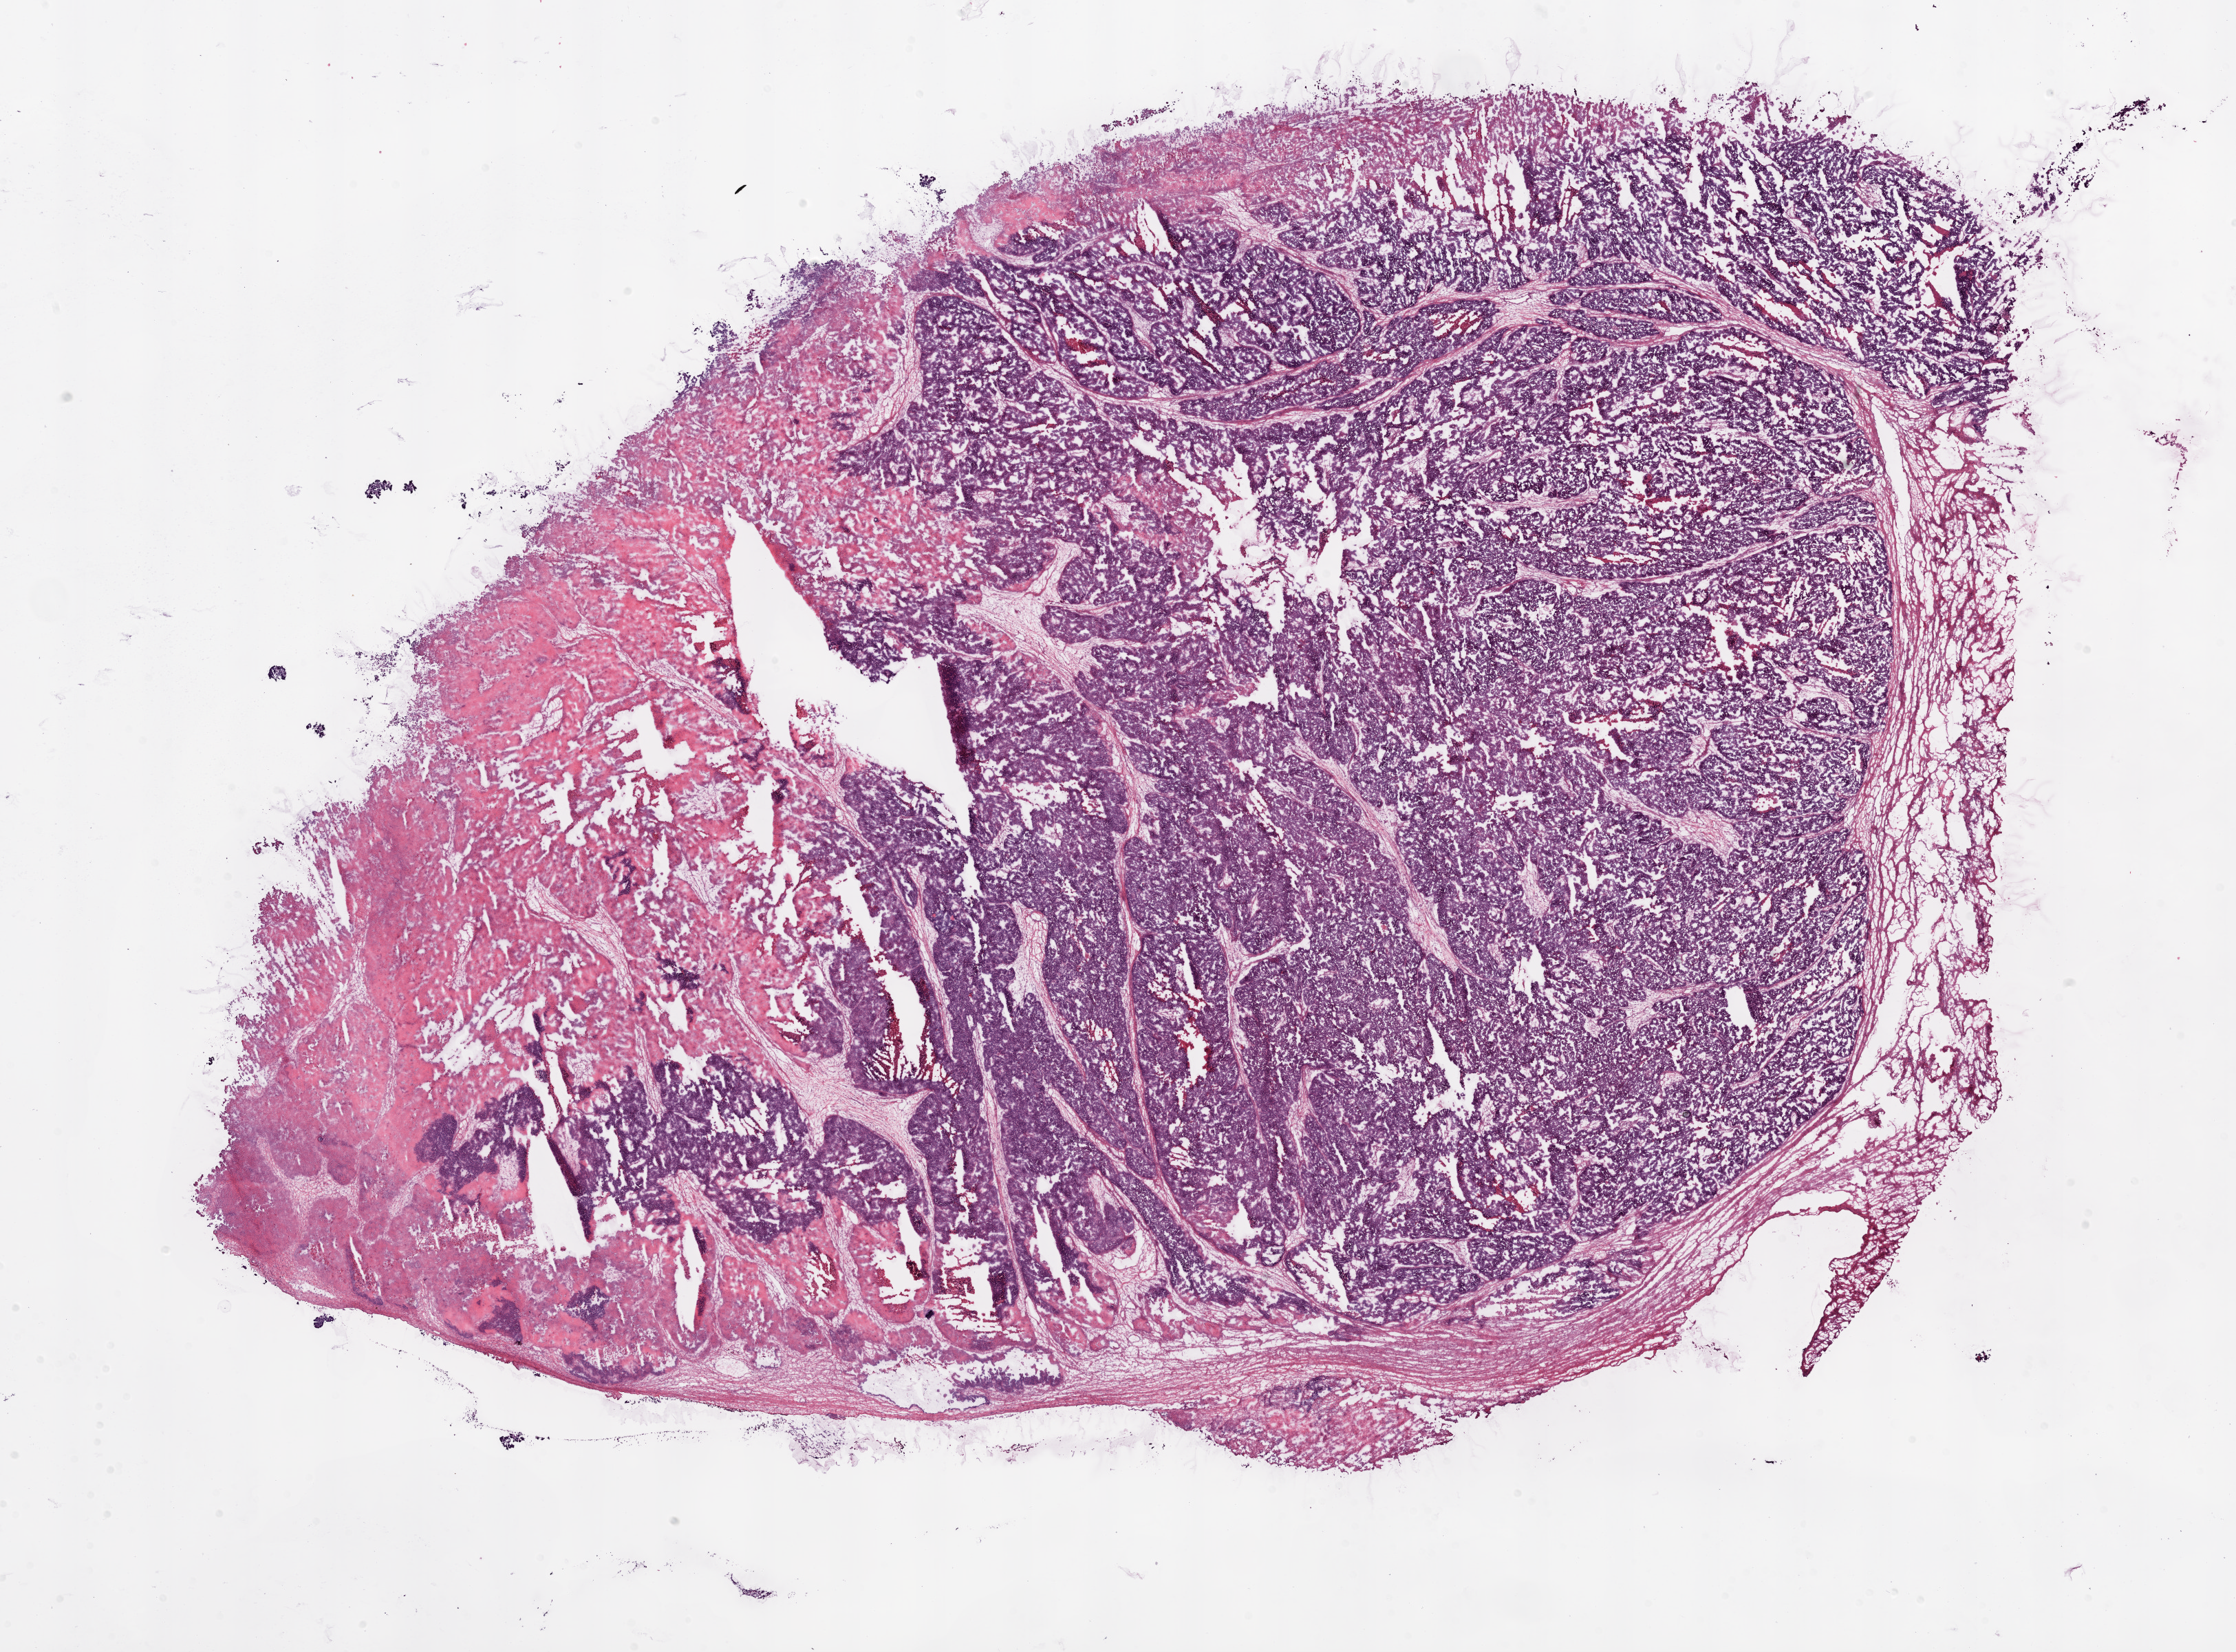
H&E whole-slide image, low-resolution overview of the scanned area, about 26.1 x 19.3 mm. Frozen section from the bottom of the tissue portion. Primary tumour sample from the ovary. Female, age 49 years at initial diagnosis. Histologic grade: G3 (poorly differentiated). Slide review estimates, as recorded: tumour cells 90%, tumour nuclei 90%, normal cells 0%, stromal cells 5%, necrosis 5%. Infiltration values recorded for this section: lymphocyte infiltration 5%, monocyte infiltration 0%, neutrophil infiltration 0%.
- laterality: bilateral
- pathologic diagnosis: Serous cystadenocarcinoma, NOS
- FIGO stage: IV